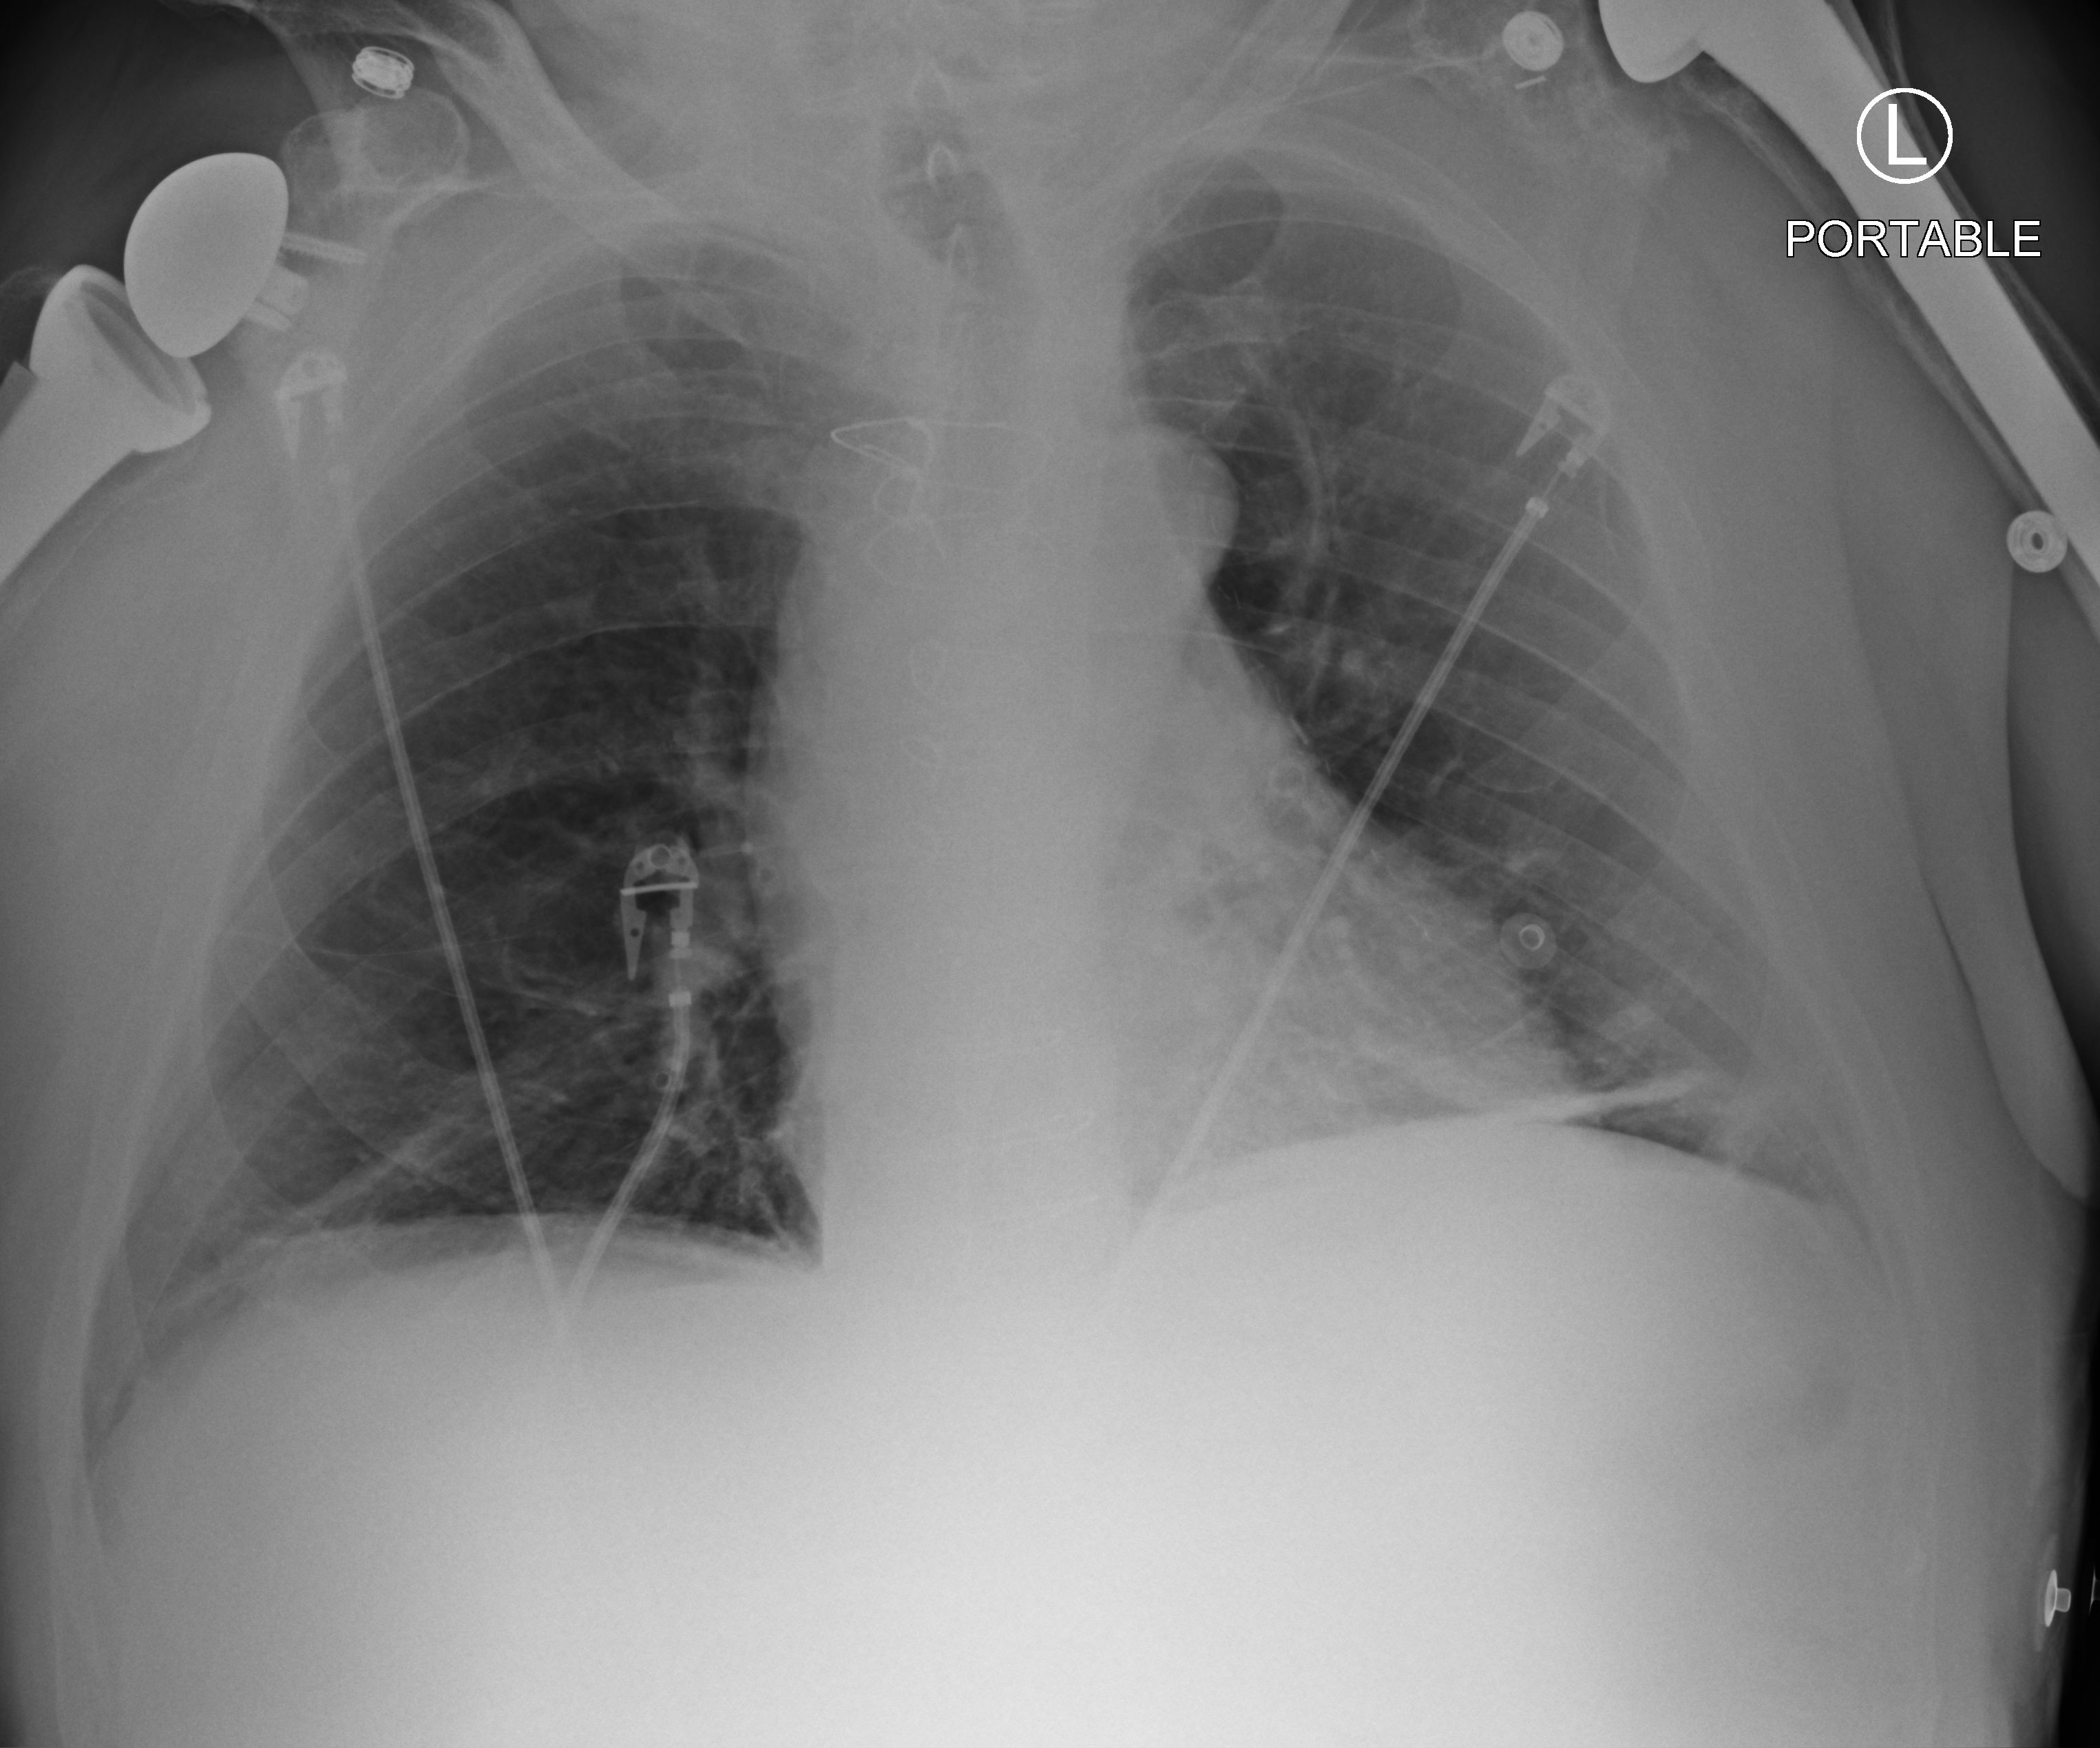
Chest X-ray (portable); anteroposterior (AP) projection. Male patient hospitalised with COVID-19, age 60–74 years.
From the hospital-stay record, not from the radiograph (when in the stay this image was taken is not recorded):
- chronic kidney disease (admission record): no
- mechanically ventilated during this hospital stay: no